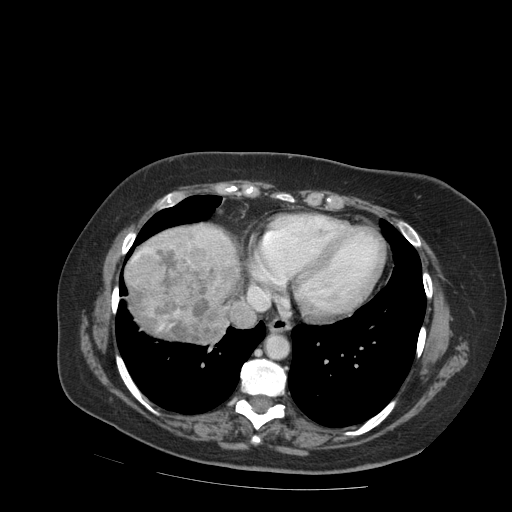
Contrast-enhanced abdominal CT (liver protocol), one axial slice. Slice 84 of 99 in the series (ordered by position). Reconstruction kernel STANDARD. 140 kVp. Soft-tissue window (W 400 / L 40 HU). 512 × 512 image matrix, field of view 400 × 400 mm. From the clinical record (not read from this slice): diagnosis: hepatocellular carcinoma (patient treated with transarterial chemoembolisation; whether this scan precedes or follows treatment is not stated here); TNM stage (as recorded): Stage-IVB; Child-Pugh class: A; tumour differentiation: moderately differentiated.
Outlined on this slice (semi-automatic segmentation, software-assisted and operator-edited):
- liver parenchyma outside the tumour (the mass and vessels are separate outlines, so this box may not span the whole liver): bounding box <124,224,240,344> (left, top, right, bottom; pixels)
- mass: <128,244,241,343>
- liver vessels: <147,236,224,250>